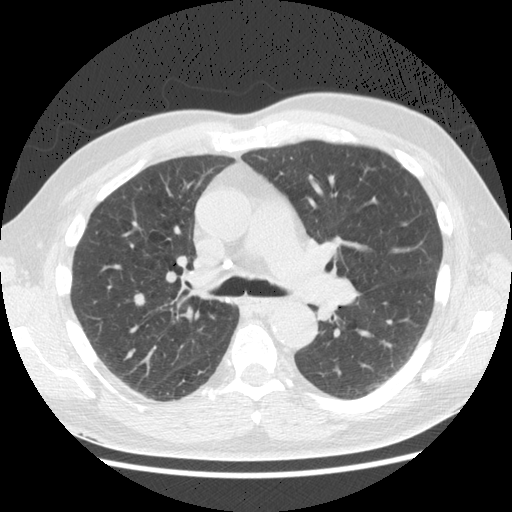
Low-dose screening chest CT, one axial slice. Position 103 of 161 along the scan axis. Reconstruction kernel STANDARD. 120 kVp. Lung window (W 1500 / L -600 HU). 2.5 mm slice thickness. 512 × 512 image matrix, field of view 360 × 360 mm.
Outlined on this slice (outlined manually by an expert reader):
- lesion 1 (tumor, upper lobe of right lung): bounding box (x1, y1, x2, y2) in pixels: (134, 294, 145, 307)